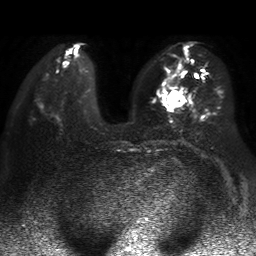
Breast MRI, one axial slice; slice 18 of 50 in the series (ordered by position); diffusion-weighted series; image 2 of 4 stored at this slice position (different b-values; order by instance number); 1.5 T; 4 mm slice thickness; 256 × 256 image matrix. Female patient.
Annotated regions visible in this slice (expert manual segmentation):
- tumour on diffusion-weighted imaging: bounding box <168,92,184,107> (left, top, right, bottom; pixels)